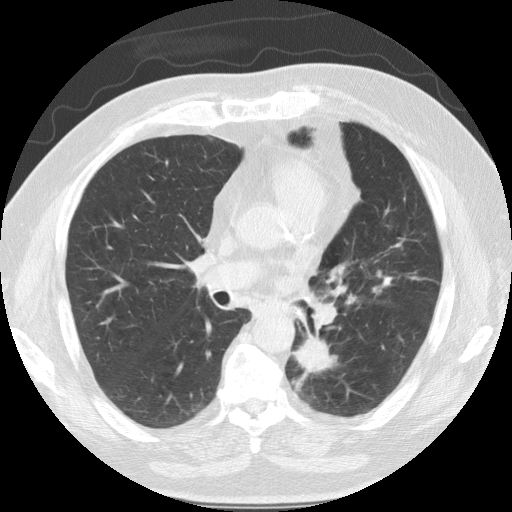
Low-dose screening chest CT, axial slice, baseline screening round, lung window (W 1500 / L -600 HU), 2.5 mm slice thickness, standard (soft-tissue) reconstruction kernel (STANDARD), 120 kVp. Male, age 68 years at enrolment. Former smoker at enrolment.
• Expert-annotated lung lesion, bounding box (x1, y1, x2, y2) in pixels: (278, 317, 352, 397).
• The screening reader recorded 3 non-calcified nodules or masses ≥4 mm on this exam (left lower lobe, lingula, right lower lobe); which of them this box marks is not recorded.